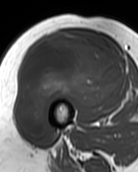
MRI of an extremity soft-tissue mass, one axial slice. Slice 54 of 99 in the series (ordered by position). MR volume resampled by the dataset authors to the PET/CT grid (not the native acquisition matrix). 3.27 mm slice thickness. 138 × 172 image matrix. Female patient. Case-level facts recorded for this patient, not image findings: histological type: pleiomorphic undifferentiated sarcoma; grade: high; site of the primary tumour: right quadricep.
Outlined on this slice (expert contour drawn on MRI and transferred to this co-registered scan by the dataset authors):
- gross tumour volume including surrounding oedema: bounding box (x1, y1, x2, y2) in pixels: (16, 32, 125, 138)
- gross tumour volume (mass): (16, 32, 125, 138)